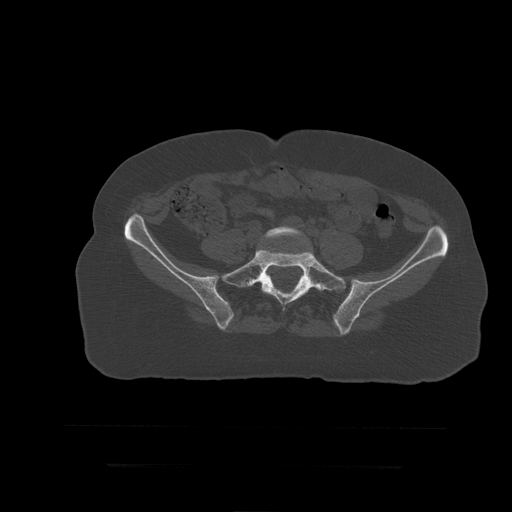
CT including the spine, one axial slice. Position 56 of 399 along the scan axis. Reconstruction kernel STANDARD. Bone window (W 1800 / L 400 HU). 512 × 512 image matrix, field of view 450 × 450 mm. Patient age 41 years. From the clinical record (not read from this slice): primary cancer: breast.
Structures marked on this image (semi-automatically segmented with operator editing):
- L5 vertebra: bounding box <264,227,313,251> (left, top, right, bottom; pixels)